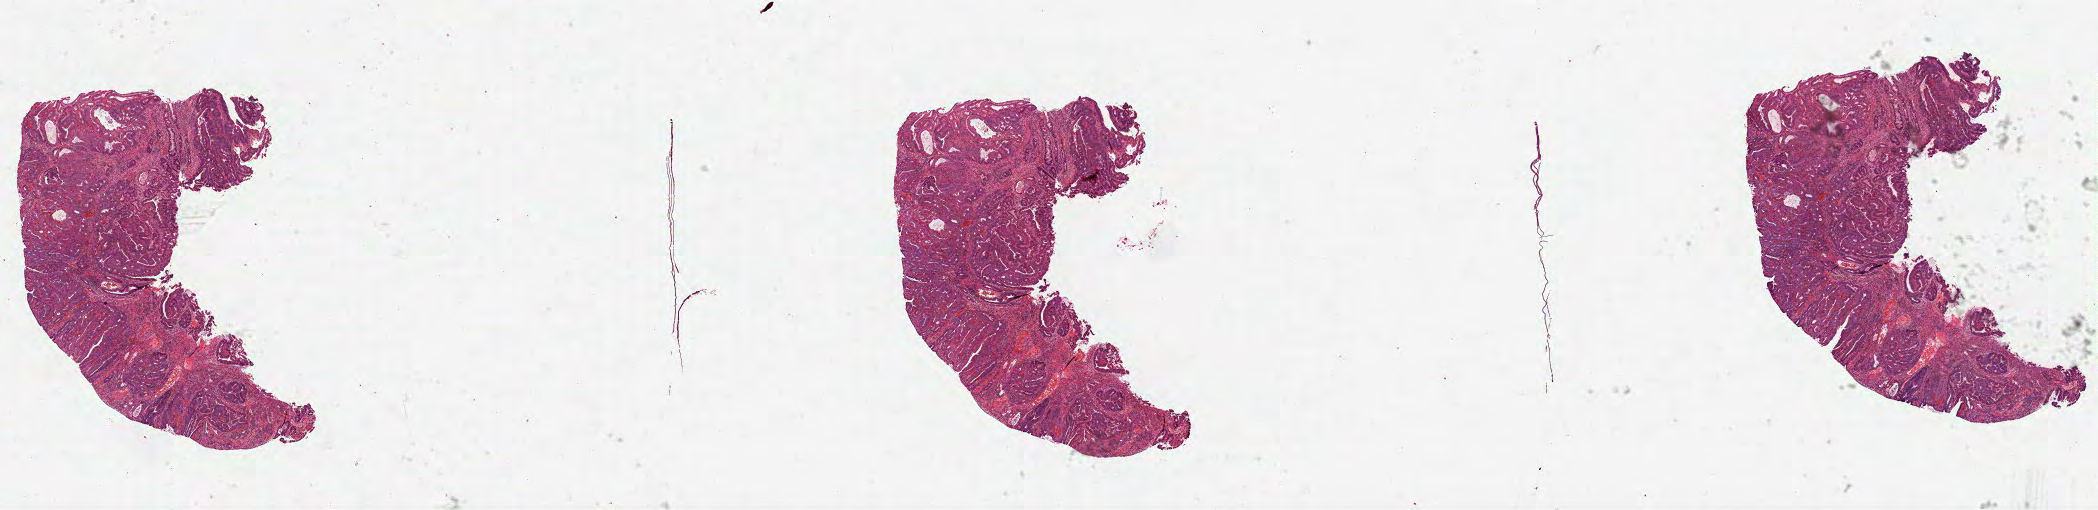
H&E whole-slide image, shown as a low-resolution overview of the whole scanned area (about 33.8 x 8.2 mm, from a 40x scan); formalin-fixed paraffin-embedded (FFPE) diagnostic section; rectum, primary tumour sample. Female patient; age at initial diagnosis 73 years.
Histologic diagnosis: Adenocarcinoma, NOS (rectosigmoid junction).